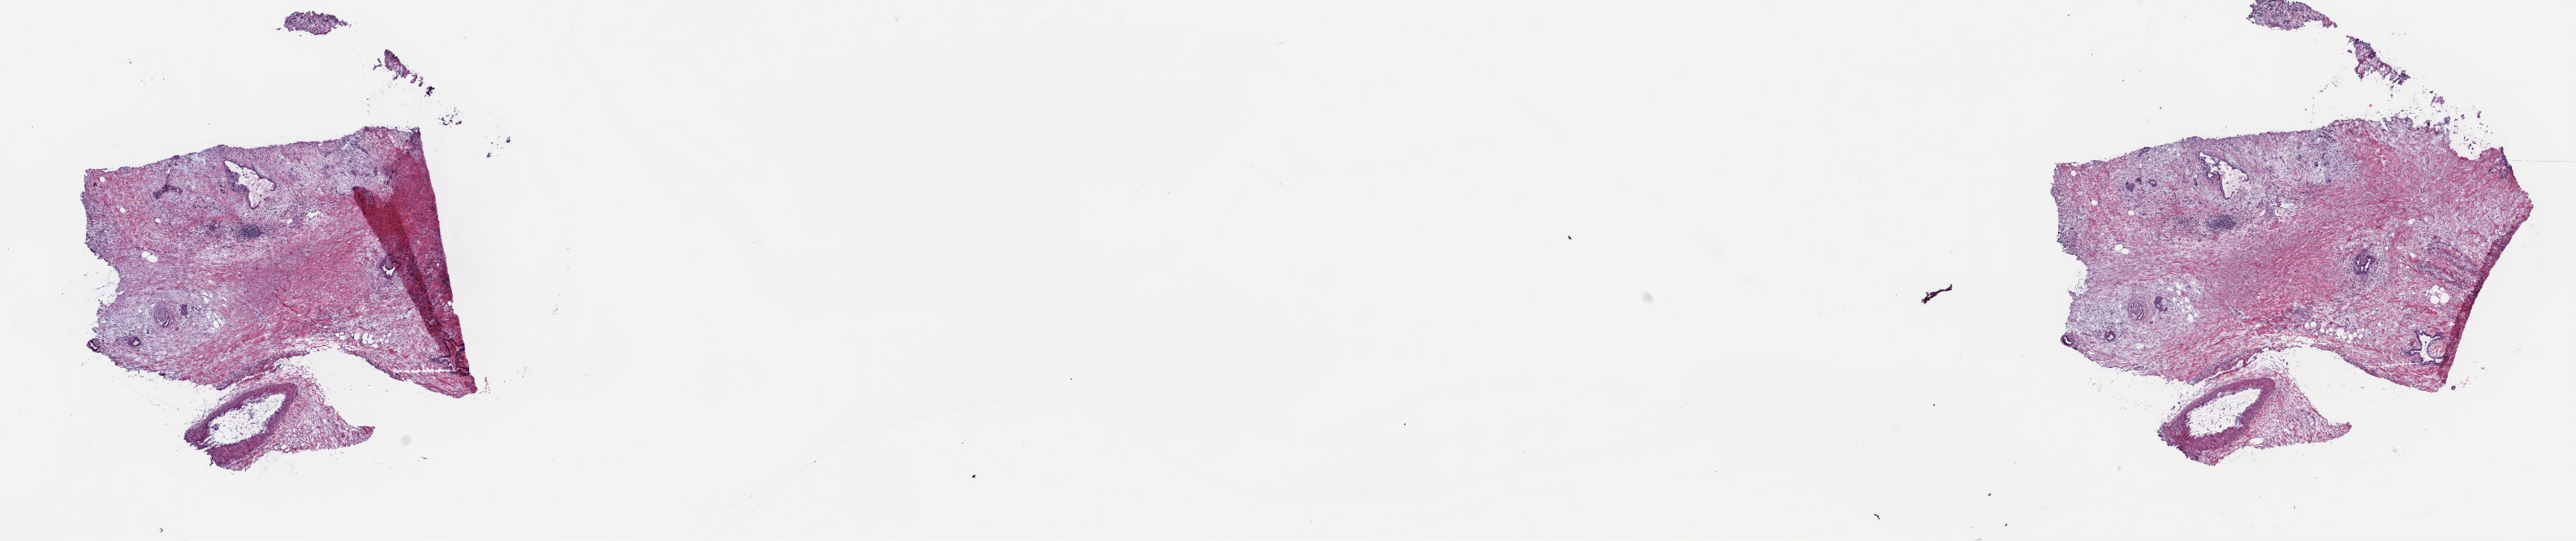
Digitized H&E tissue section (whole slide) — shown as a low-resolution overview of the whole scanned area (about 25.7 x 5.4 mm), frozen section, pancreas, primary tumour sample. Male patient; age at initial diagnosis 66 years. Histologic grade: G3 (poorly differentiated). Composition of this section per pathologist review: tumour cells 5%, tumour nuclei 10%, normal cells 15%, stromal cells 80%, necrosis 0%. Infiltration values recorded for this section: lymphocyte infiltration 0%, monocyte infiltration 0%, neutrophil infiltration 0%.
• AJCC pathologic stage: IIB
• TNM: T3 N1 MX
• pathologic diagnosis: Infiltrating duct carcinoma, NOS (head of pancreas)